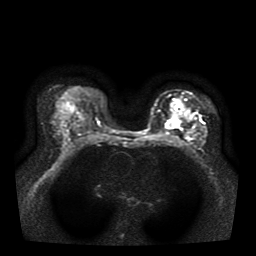
Breast MRI, one axial slice. Slice 23 of 39 in the series (ordered by position). Diffusion-weighted series; image 2 of 4 stored at this slice position (different b-values; order by instance number). 1.5 T. 256 × 256 image matrix. Female patient.
Outlined on this slice (expert manual segmentation):
- tumour on diffusion-weighted imaging: bounding box <166,109,193,129> (left, top, right, bottom; pixels)